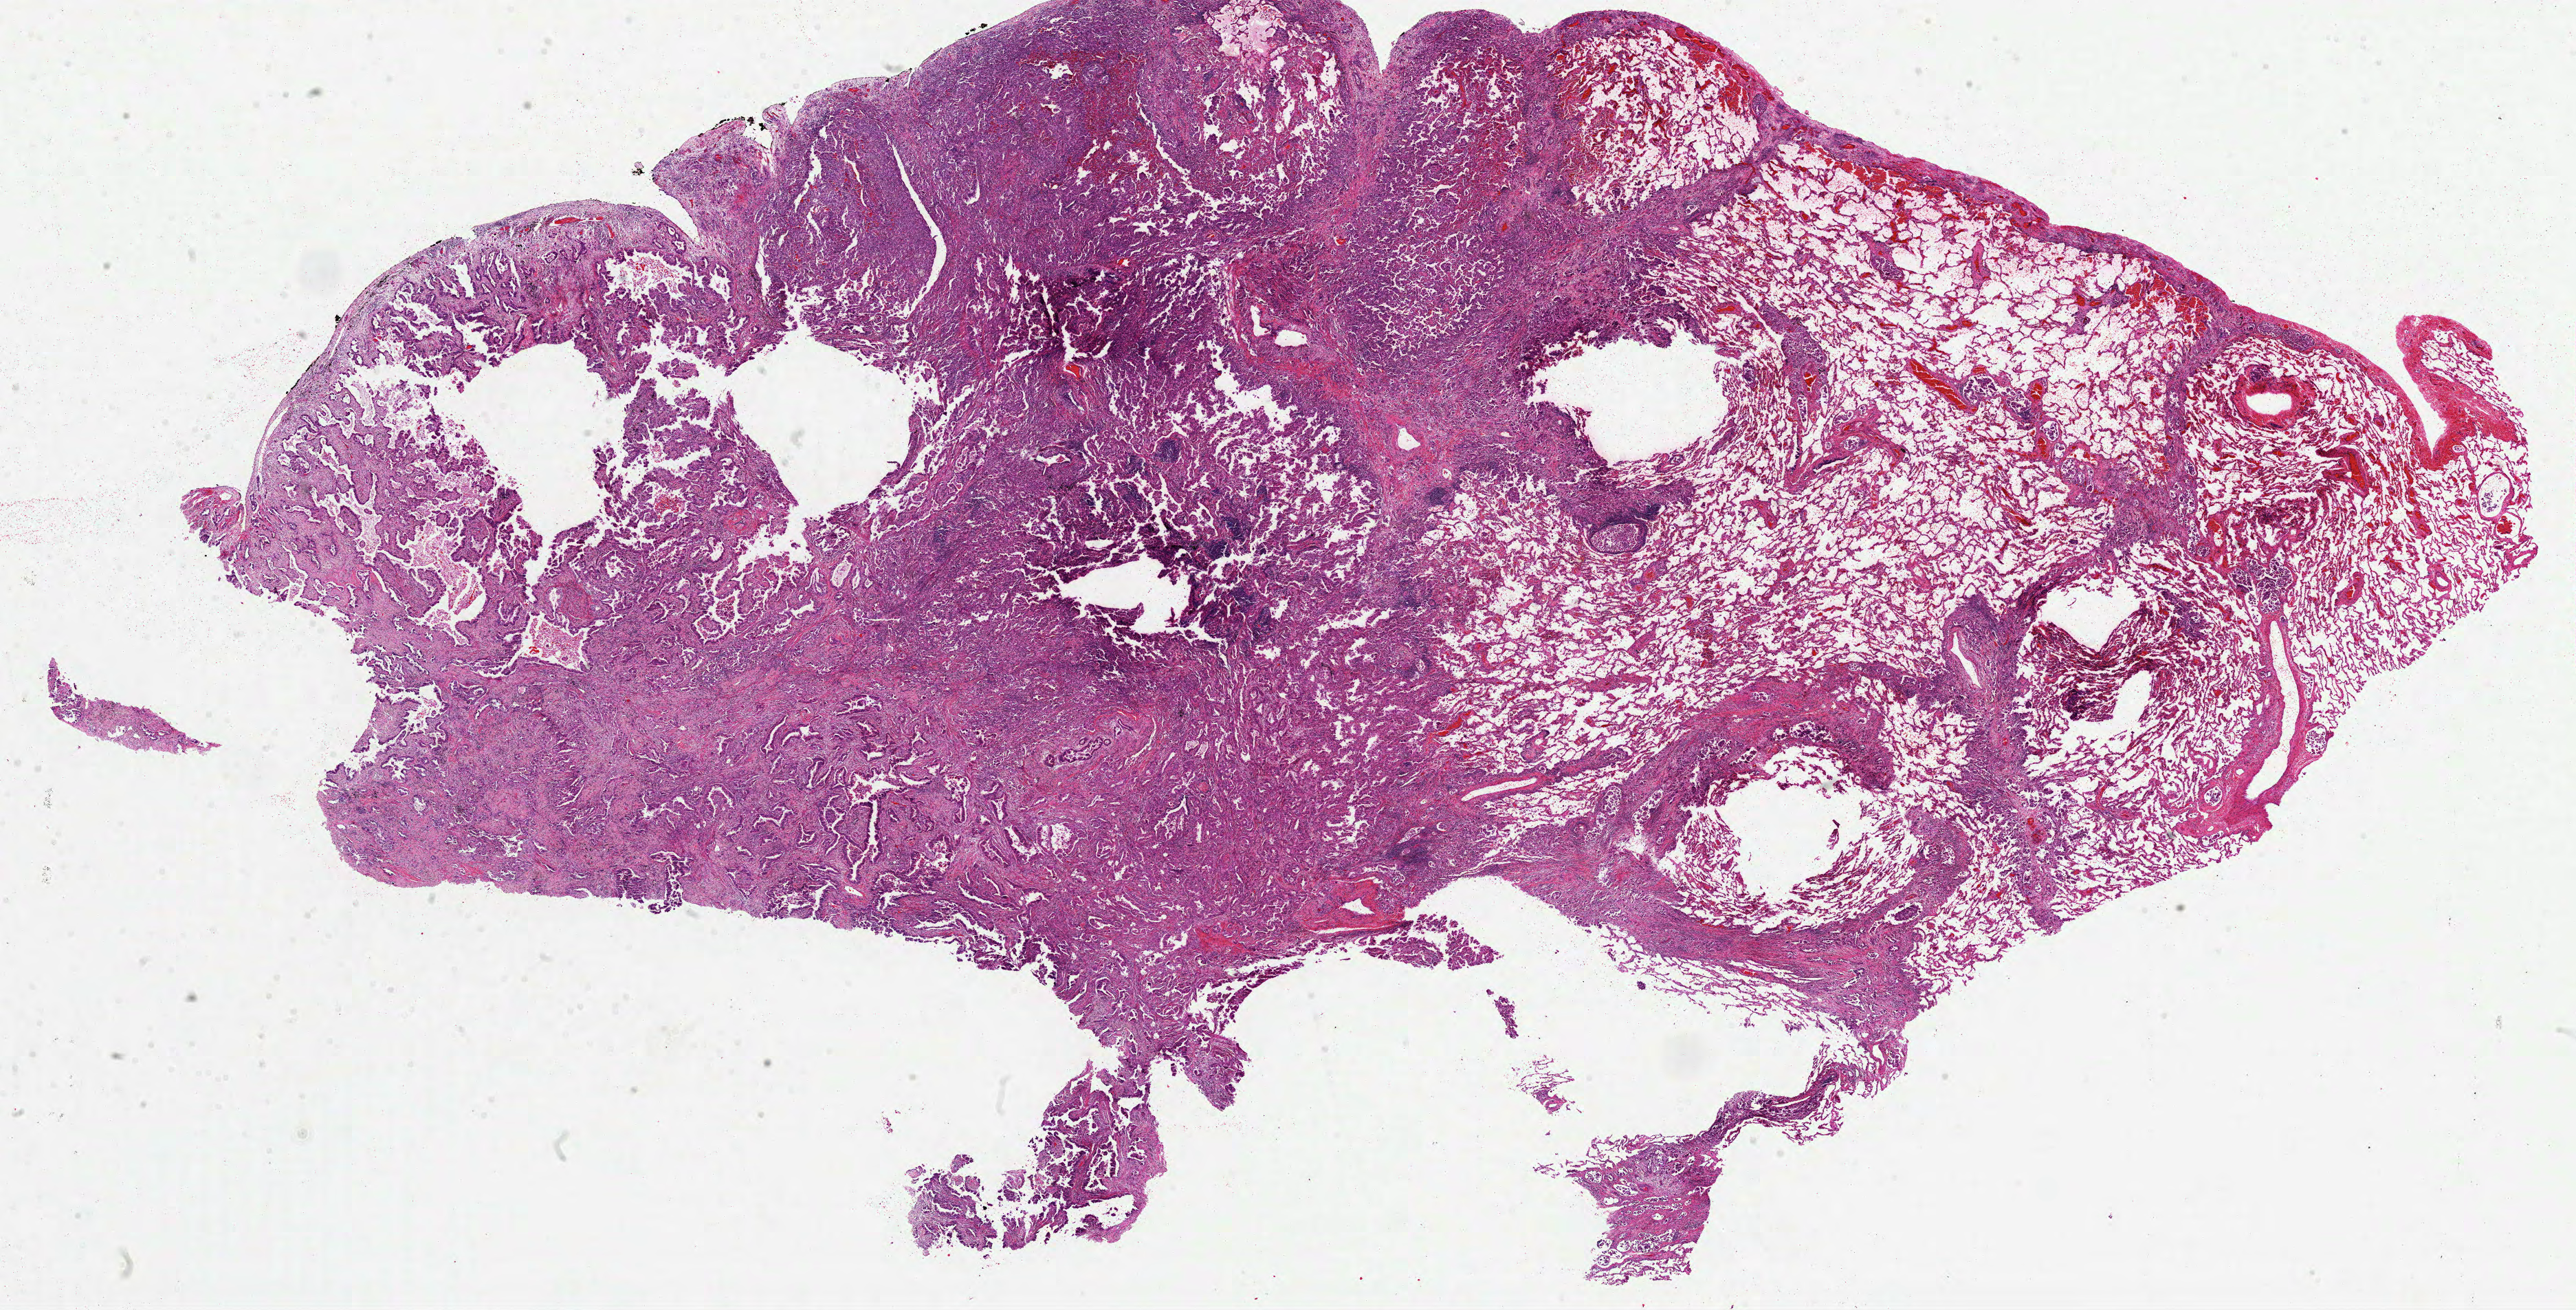
Whole-slide histology image, H&E — whole scanned area (about 30.2 x 15.4 mm, slide scanned at 40x) shown as a low-resolution overview, FFPE section, lung, primary tumour sample. Female patient; age at initial diagnosis 45 years.
* pathologic diagnosis: Adenocarcinoma, NOS (upper lobe, lung)
* laterality: left
* AJCC pathologic stage: IIIA
* TNM: T3 N2 M0